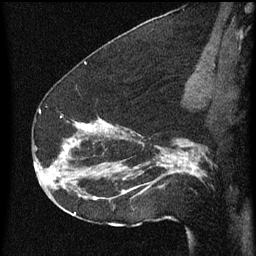
Breast MRI (dynamic contrast-enhanced), one sagittal slice. Slice 36 of 60 in the series (ordered by position). Dynamic contrast-enhanced series, image 2 of 3 at this slice position (ordered by acquisition). 1.5 T. TE 4.2 ms, TR 8 ms. 2 mm slice thickness. 256 × 256 image matrix, field of view 180 × 180 mm. Female patient, age 52 years.
Outlined on this slice (semi-automatic segmentation, software-assisted and operator-edited):
- analysis volume of interest (the breast-tissue region the enhancement analysis was run in; not a lesion): box from (x=54, y=114) to (x=178, y=207) px
- tumour enhancement mask (voxels above the 70 % enhancement threshold inside the analysis volume of interest): (x=60, y=124)–(x=178, y=199)